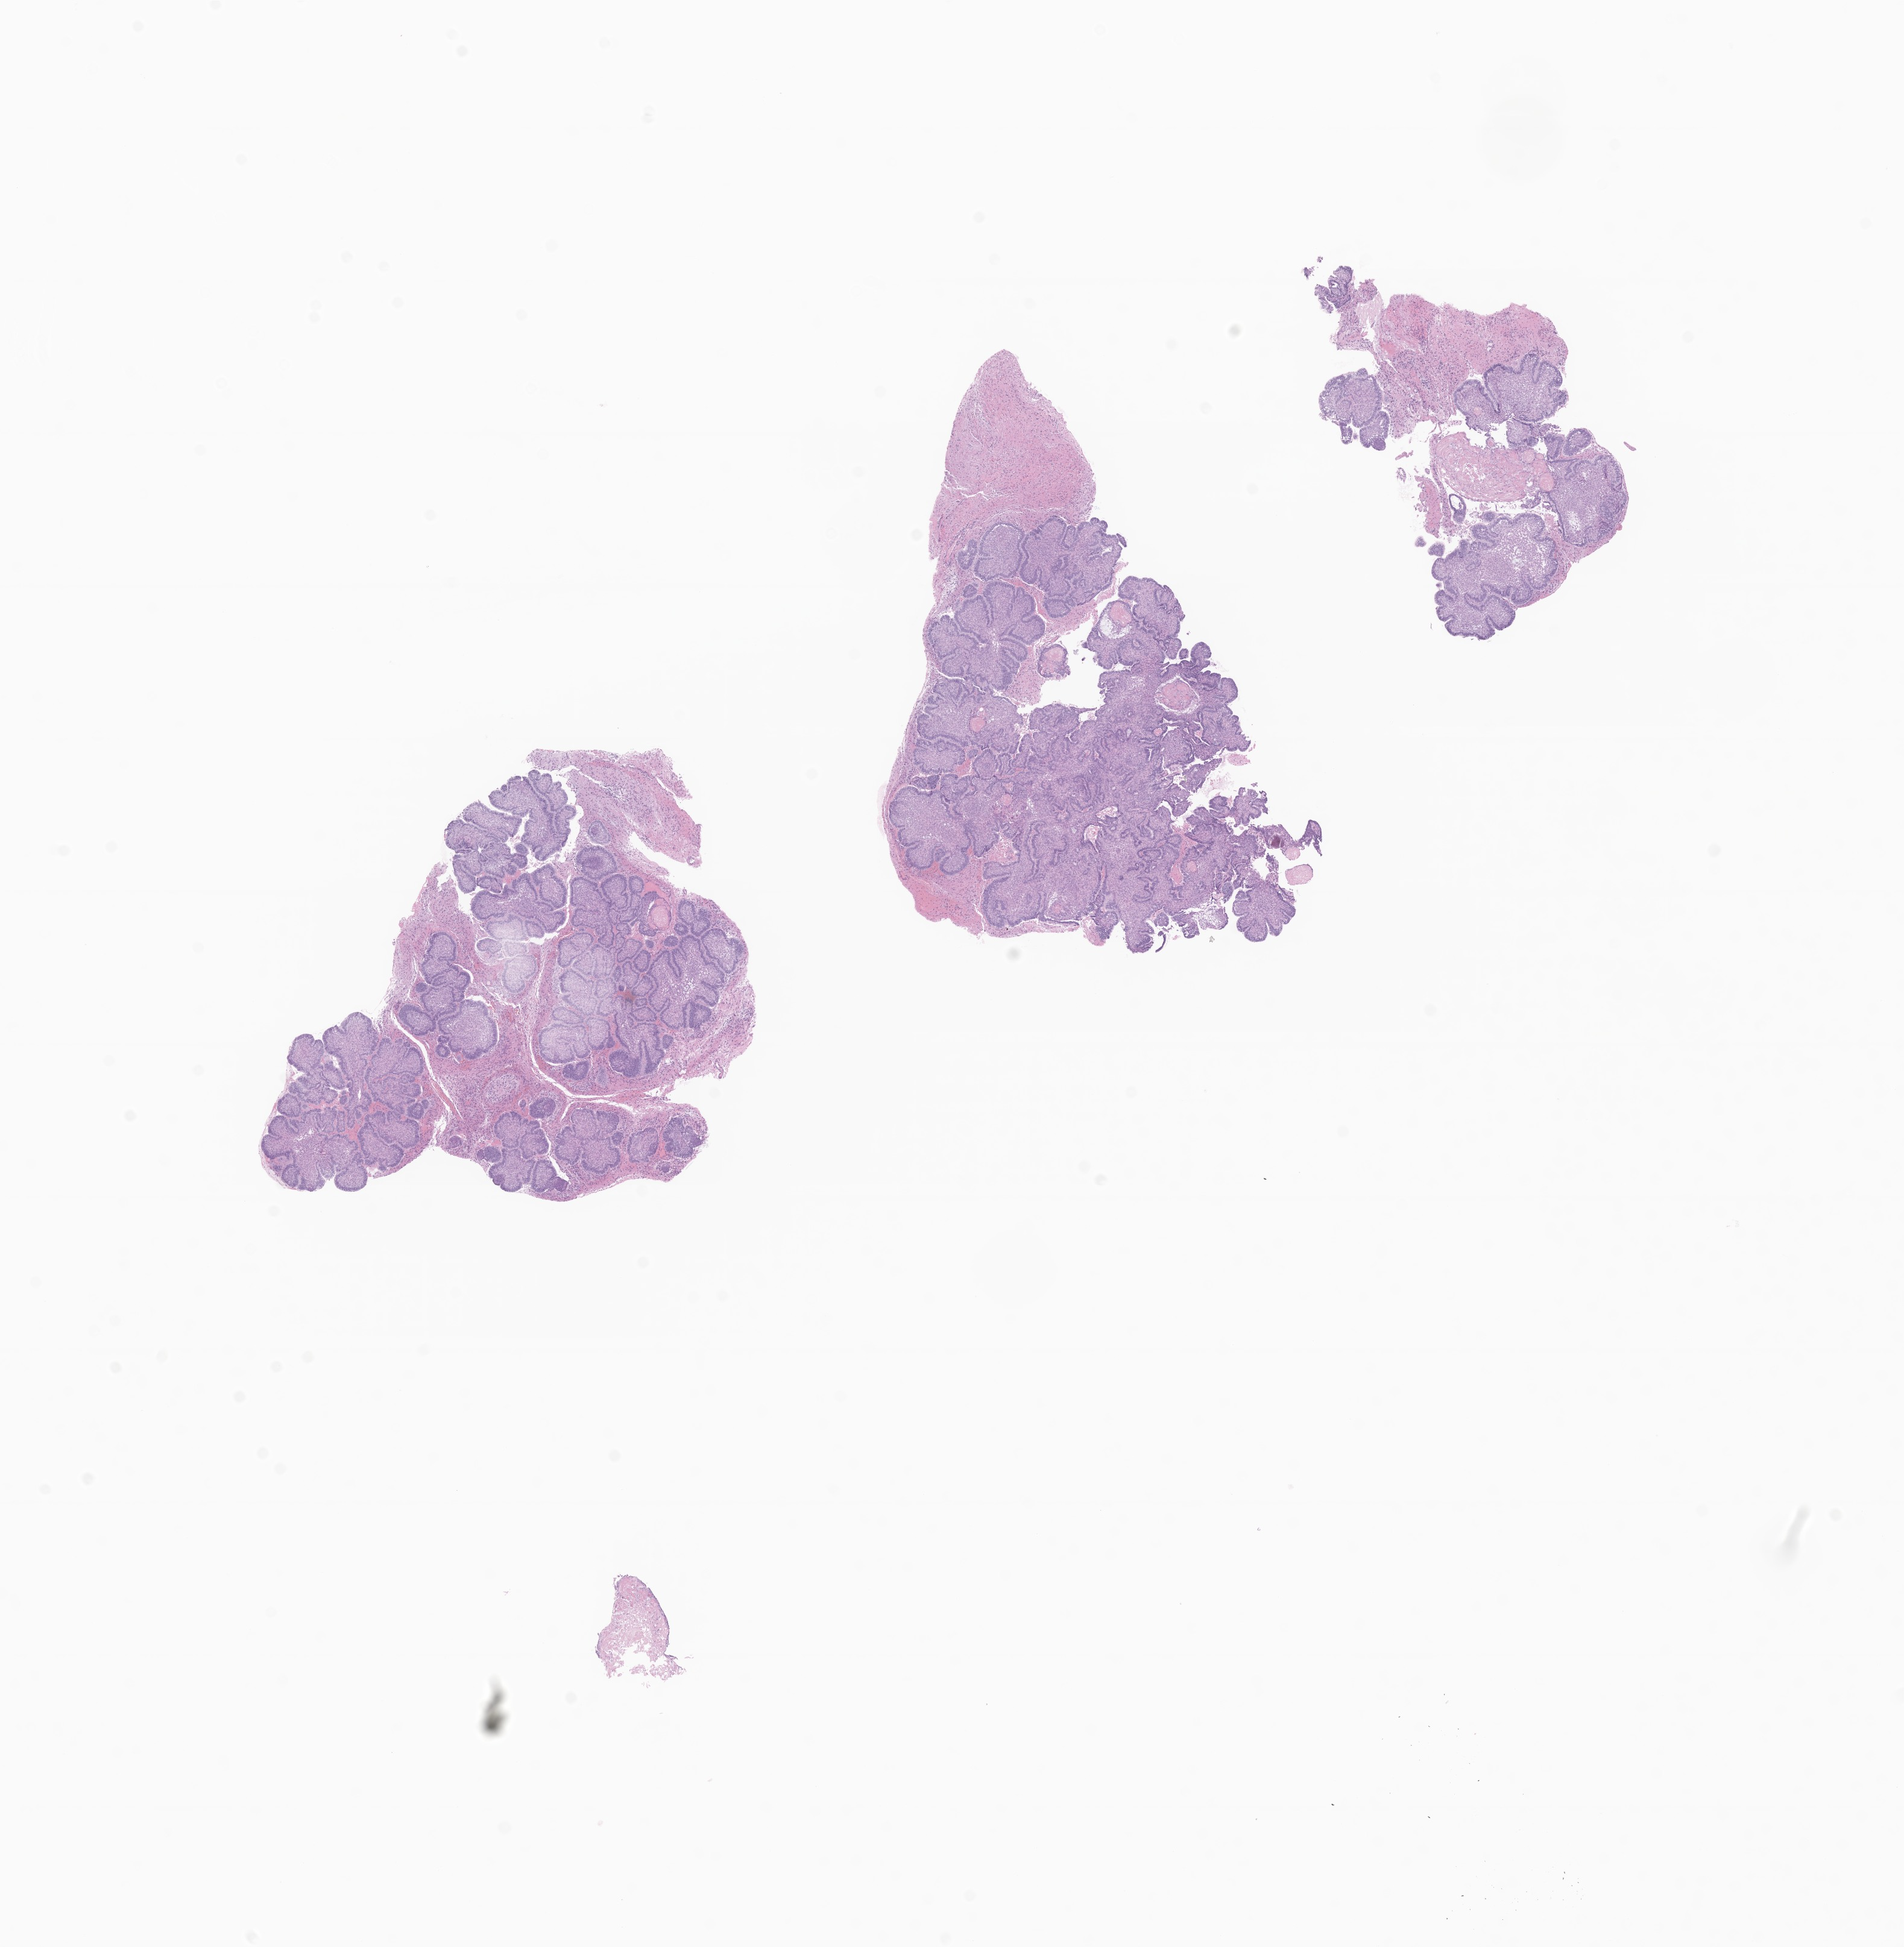
Whole-slide image, haematoxylin and eosin stain of tumor tissue from the brain — shown as a low-resolution overview of the whole scanned area (about 13.3 x 13.6 mm). Formalin-fixed paraffin-embedded section. Female patient, age 187 months (15 years 7 months).
Diagnosis: Neoplasm, malignant.